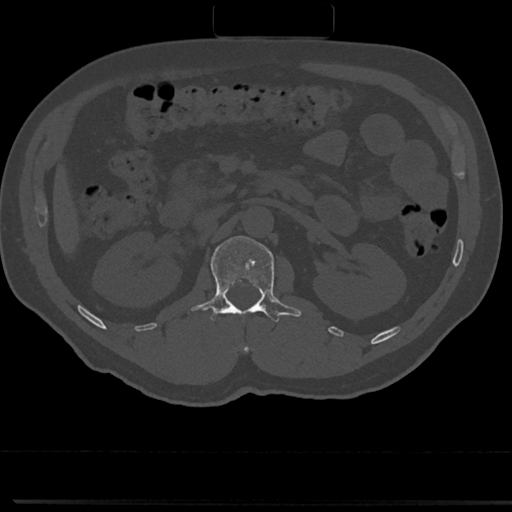
CT including the spine, one axial slice; 120 kVp; bone window (W 1800 / L 400 HU); 0.5 mm slice thickness; 512 × 512 image matrix. Male patient, age 61 years. From the clinical record (not read from this slice): primary cancer: prostate.
Outlined on this slice (semi-automatically segmented with operator editing):
- L1 vertebra: bounding box [x1, y1, x2, y2] px = [191, 237, 300, 323]